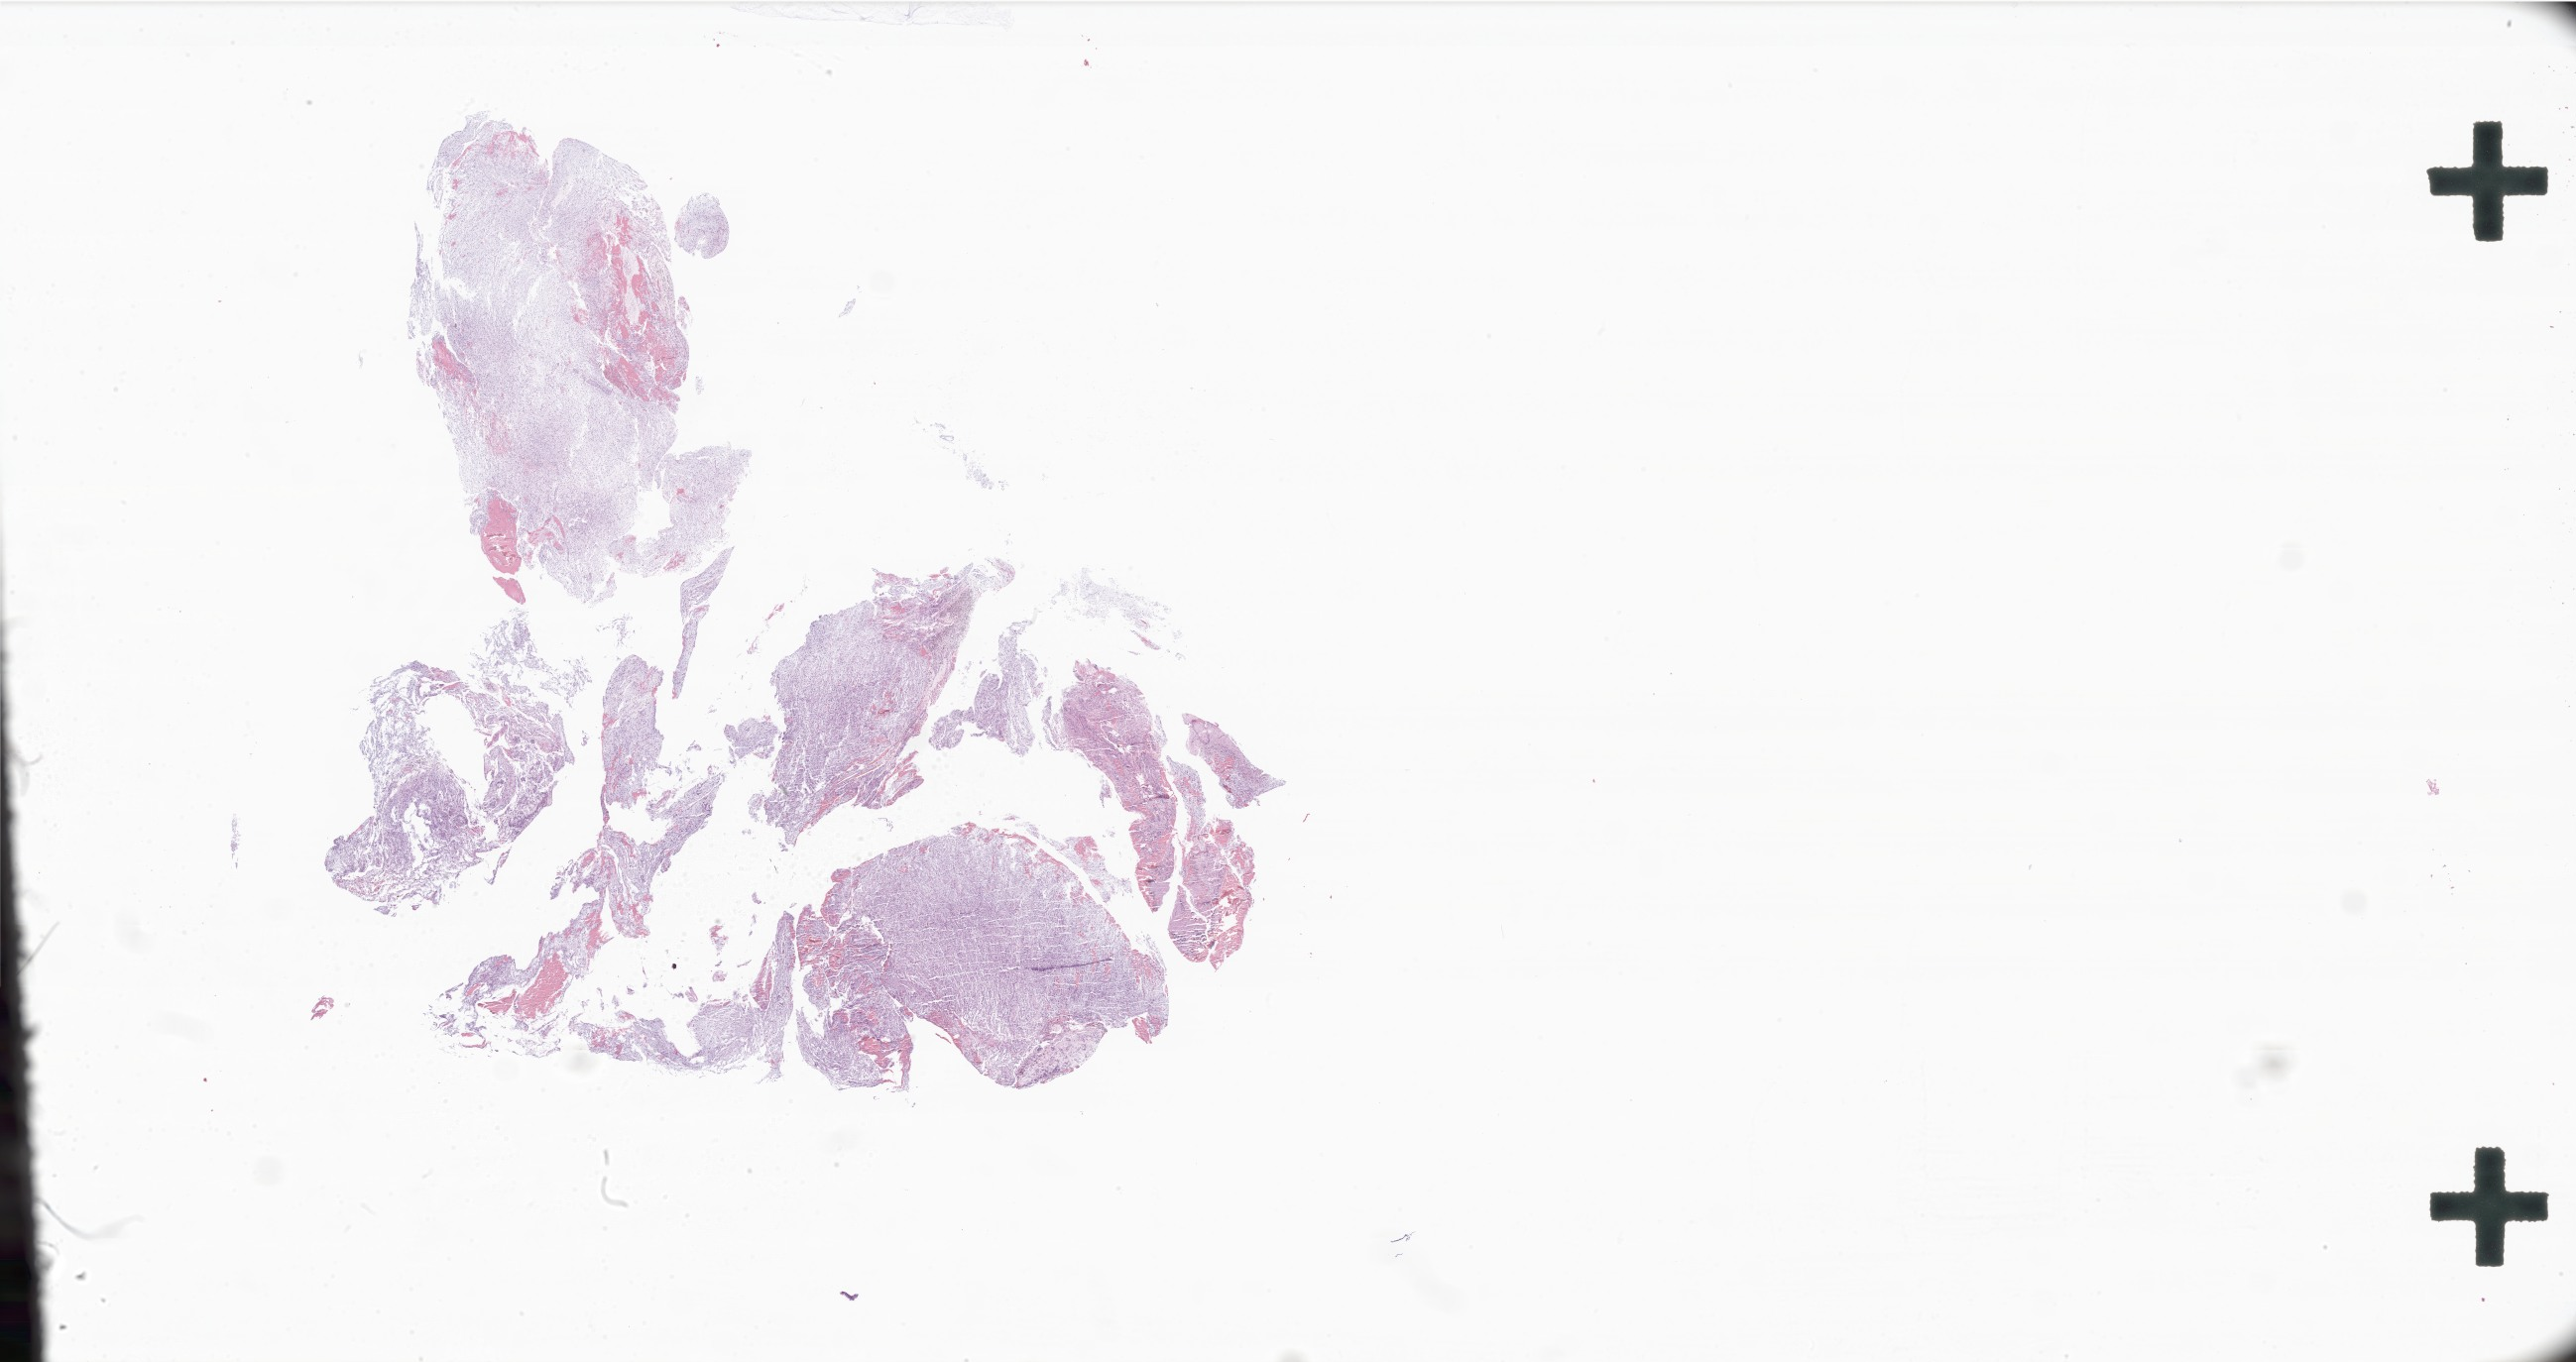
Digitized hematoxylin and eosin (H&E)-stained section of tumor tissue from the brain — low-resolution overview of the scanned area, about 43.8 x 23.2 mm. Formalin-fixed, paraffin-embedded (FFPE) tissue. Male patient, age 132 months (11 years).
Recorded diagnosis: Astrocytoma, NOS.